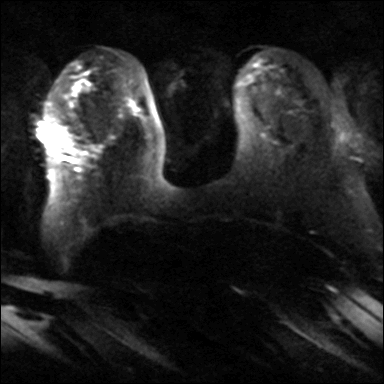
Breast MRI, one axial slice; diffusion-weighted series; image 2 of 4 stored at this slice position (different b-values; order by instance number); 3 T; 4 mm slice thickness; 384 × 384 image matrix, field of view 320 × 320 mm. Female patient.
Structures marked on this image (manually delineated by an expert):
- tumour on diffusion-weighted imaging: bounding box (x1, y1, x2, y2) in pixels: (54, 133, 66, 143)